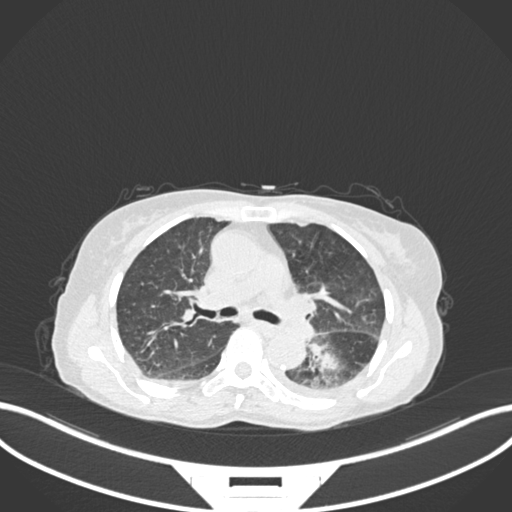
Chest CT, one axial slice. Position 109 of 233 along the scan axis. Lung window (W 1500 / L -600 HU). 512 × 512 image matrix, field of view 400 × 400 mm. Female patient, age 78 years. From the clinical record (not read from this slice): clinical TNM (as recorded): T3 N0 M1.
Annotated regions visible in this slice (rectangle marked by the reading radiologist):
- lung tumour (recorded histology: squamous cell carcinoma): bounding box (x1, y1, x2, y2) in pixels: (301, 328, 362, 396)